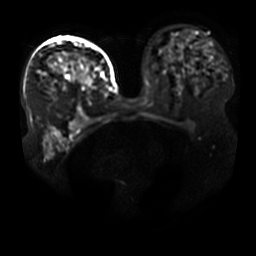
Breast MRI, one axial slice; position 26 of 41 along the scan axis; diffusion-weighted series; image 2 of 4 stored at this slice position (different b-values; order by instance number); 3 T; 5 mm slice thickness; 256 × 256 image matrix. Female patient.
Annotated regions visible in this slice (outlined manually by an expert reader):
- tumour on diffusion-weighted imaging: bounding box (x1, y1, x2, y2) in pixels: (49, 59, 96, 87)